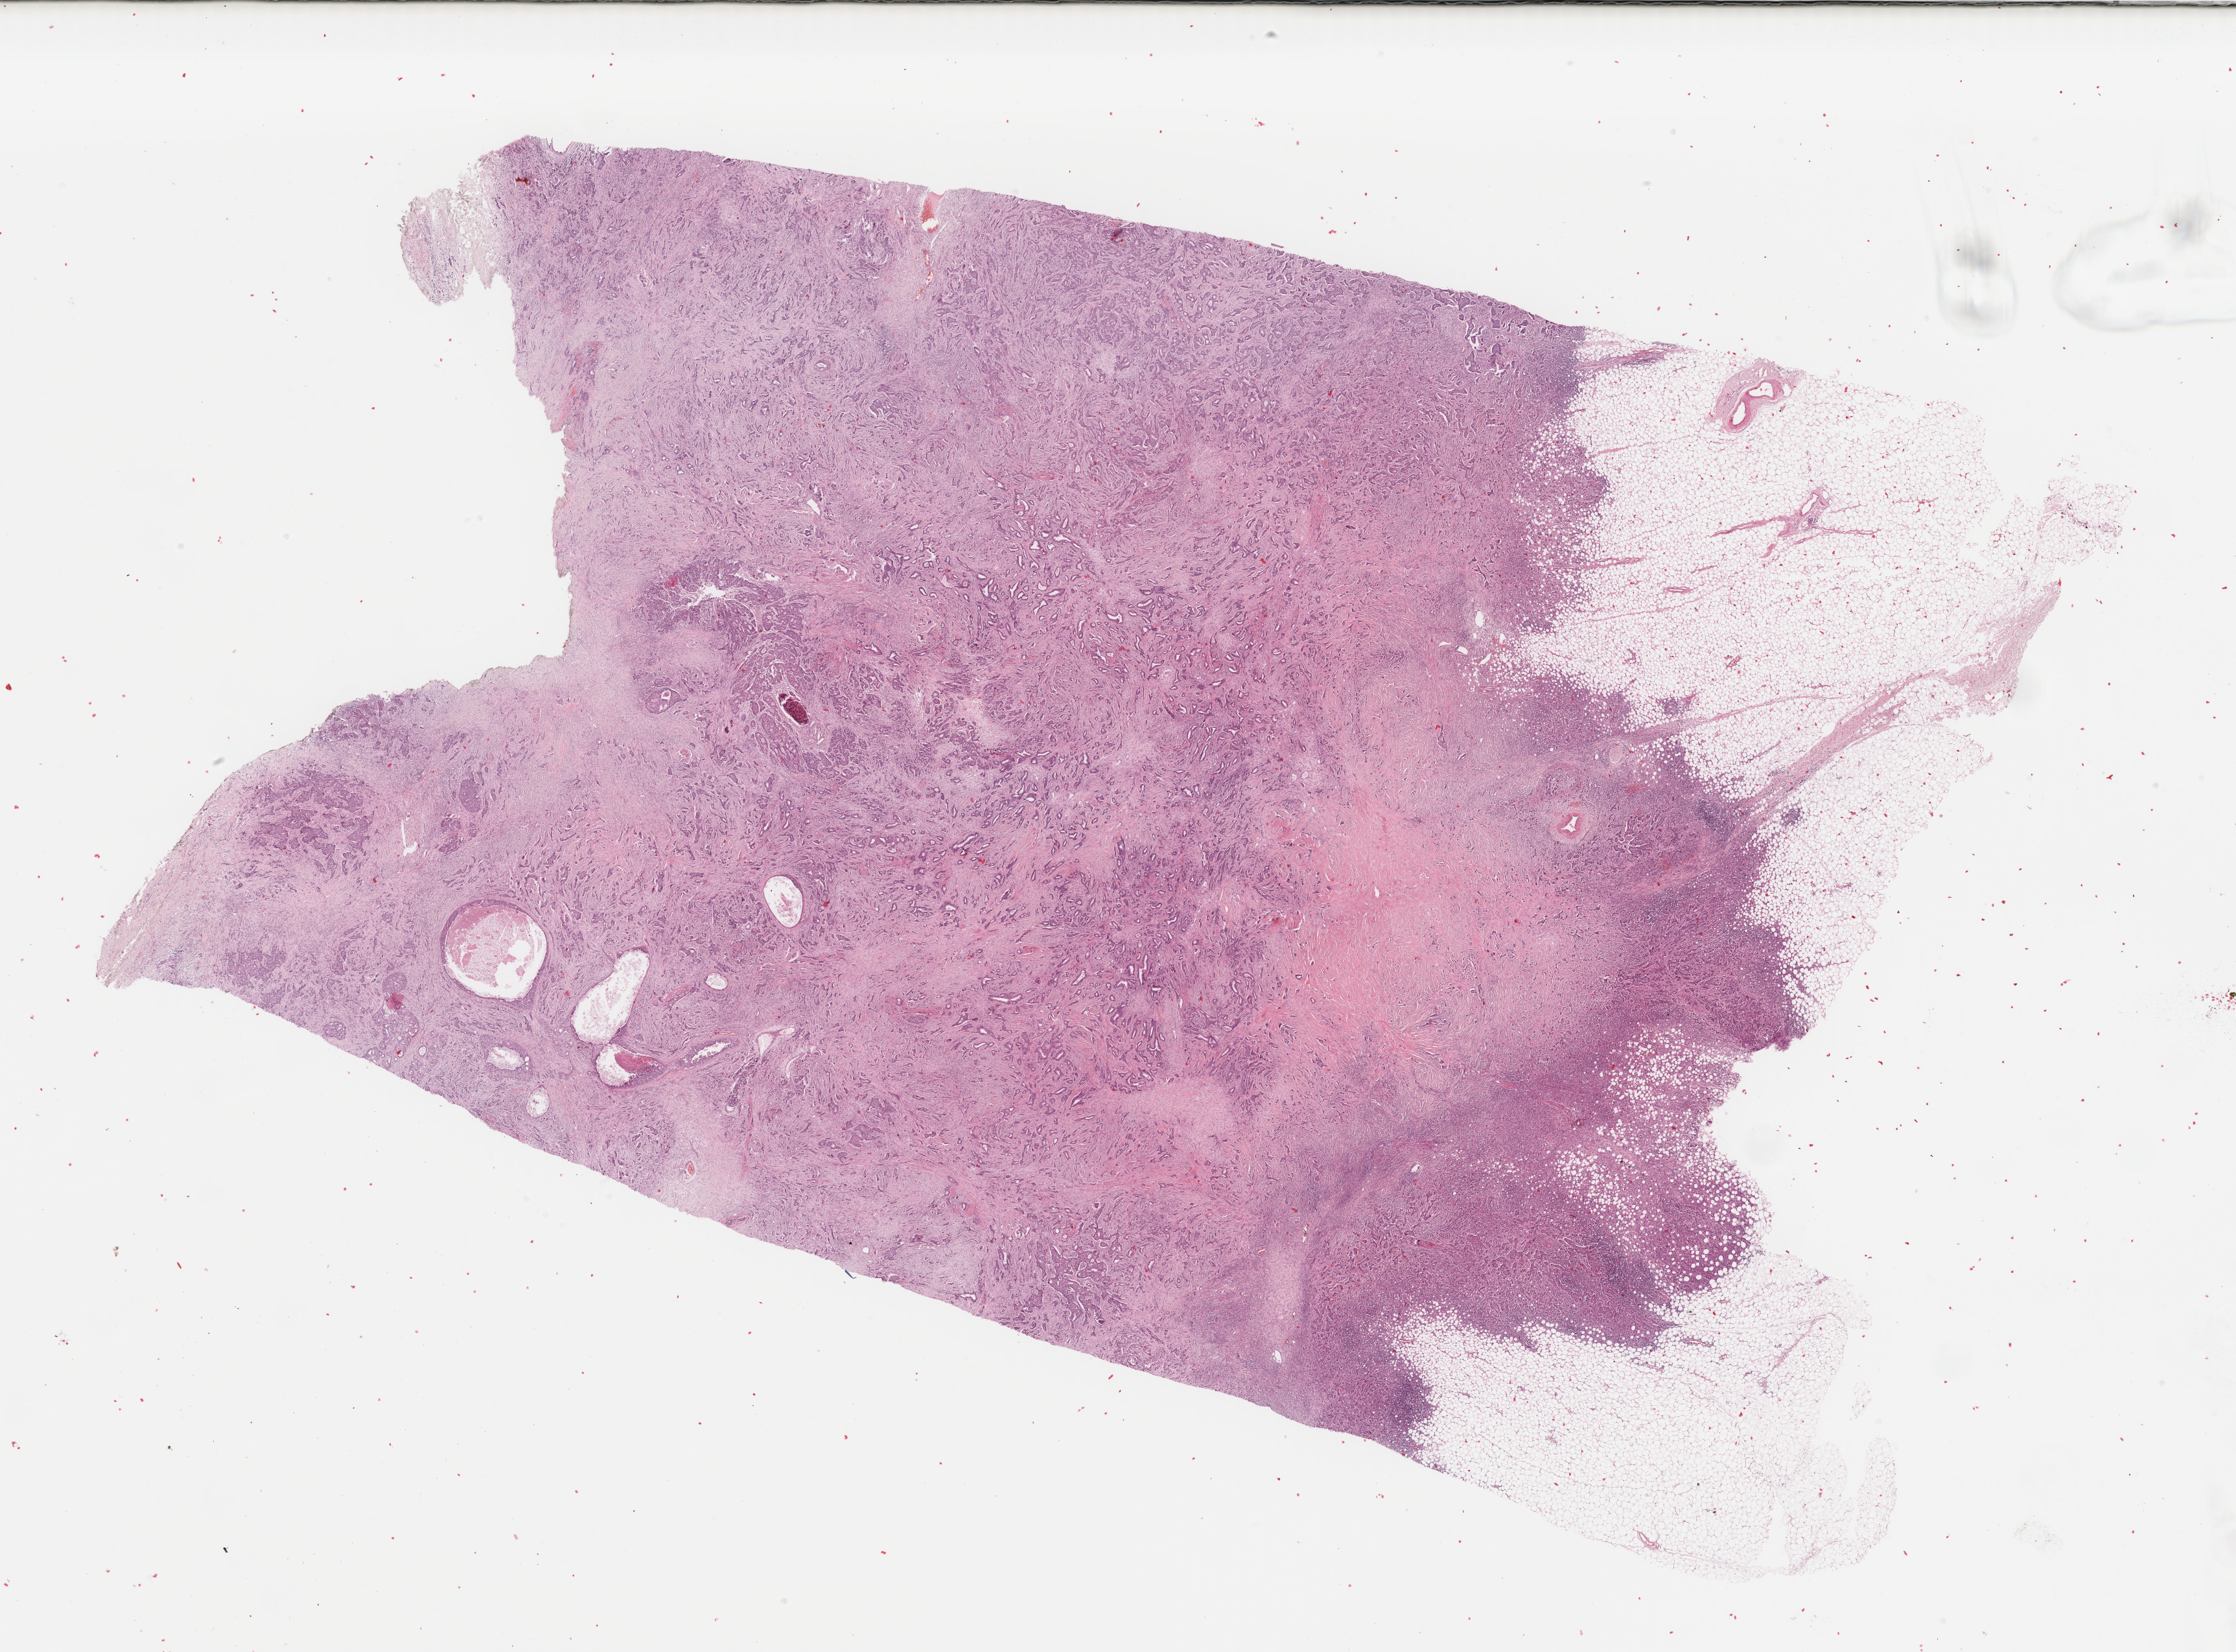
Hematoxylin and eosin (H&E) stained whole-slide image, a low-resolution overview of the entire scanned area, about 27.4 x 20.2 mm (from a 40x scan). Formalin-fixed paraffin-embedded (FFPE) diagnostic section. Breast, primary tumour sample. Female patient; age at initial diagnosis 41 years.
Diagnosis: Infiltrating duct carcinoma, NOS.